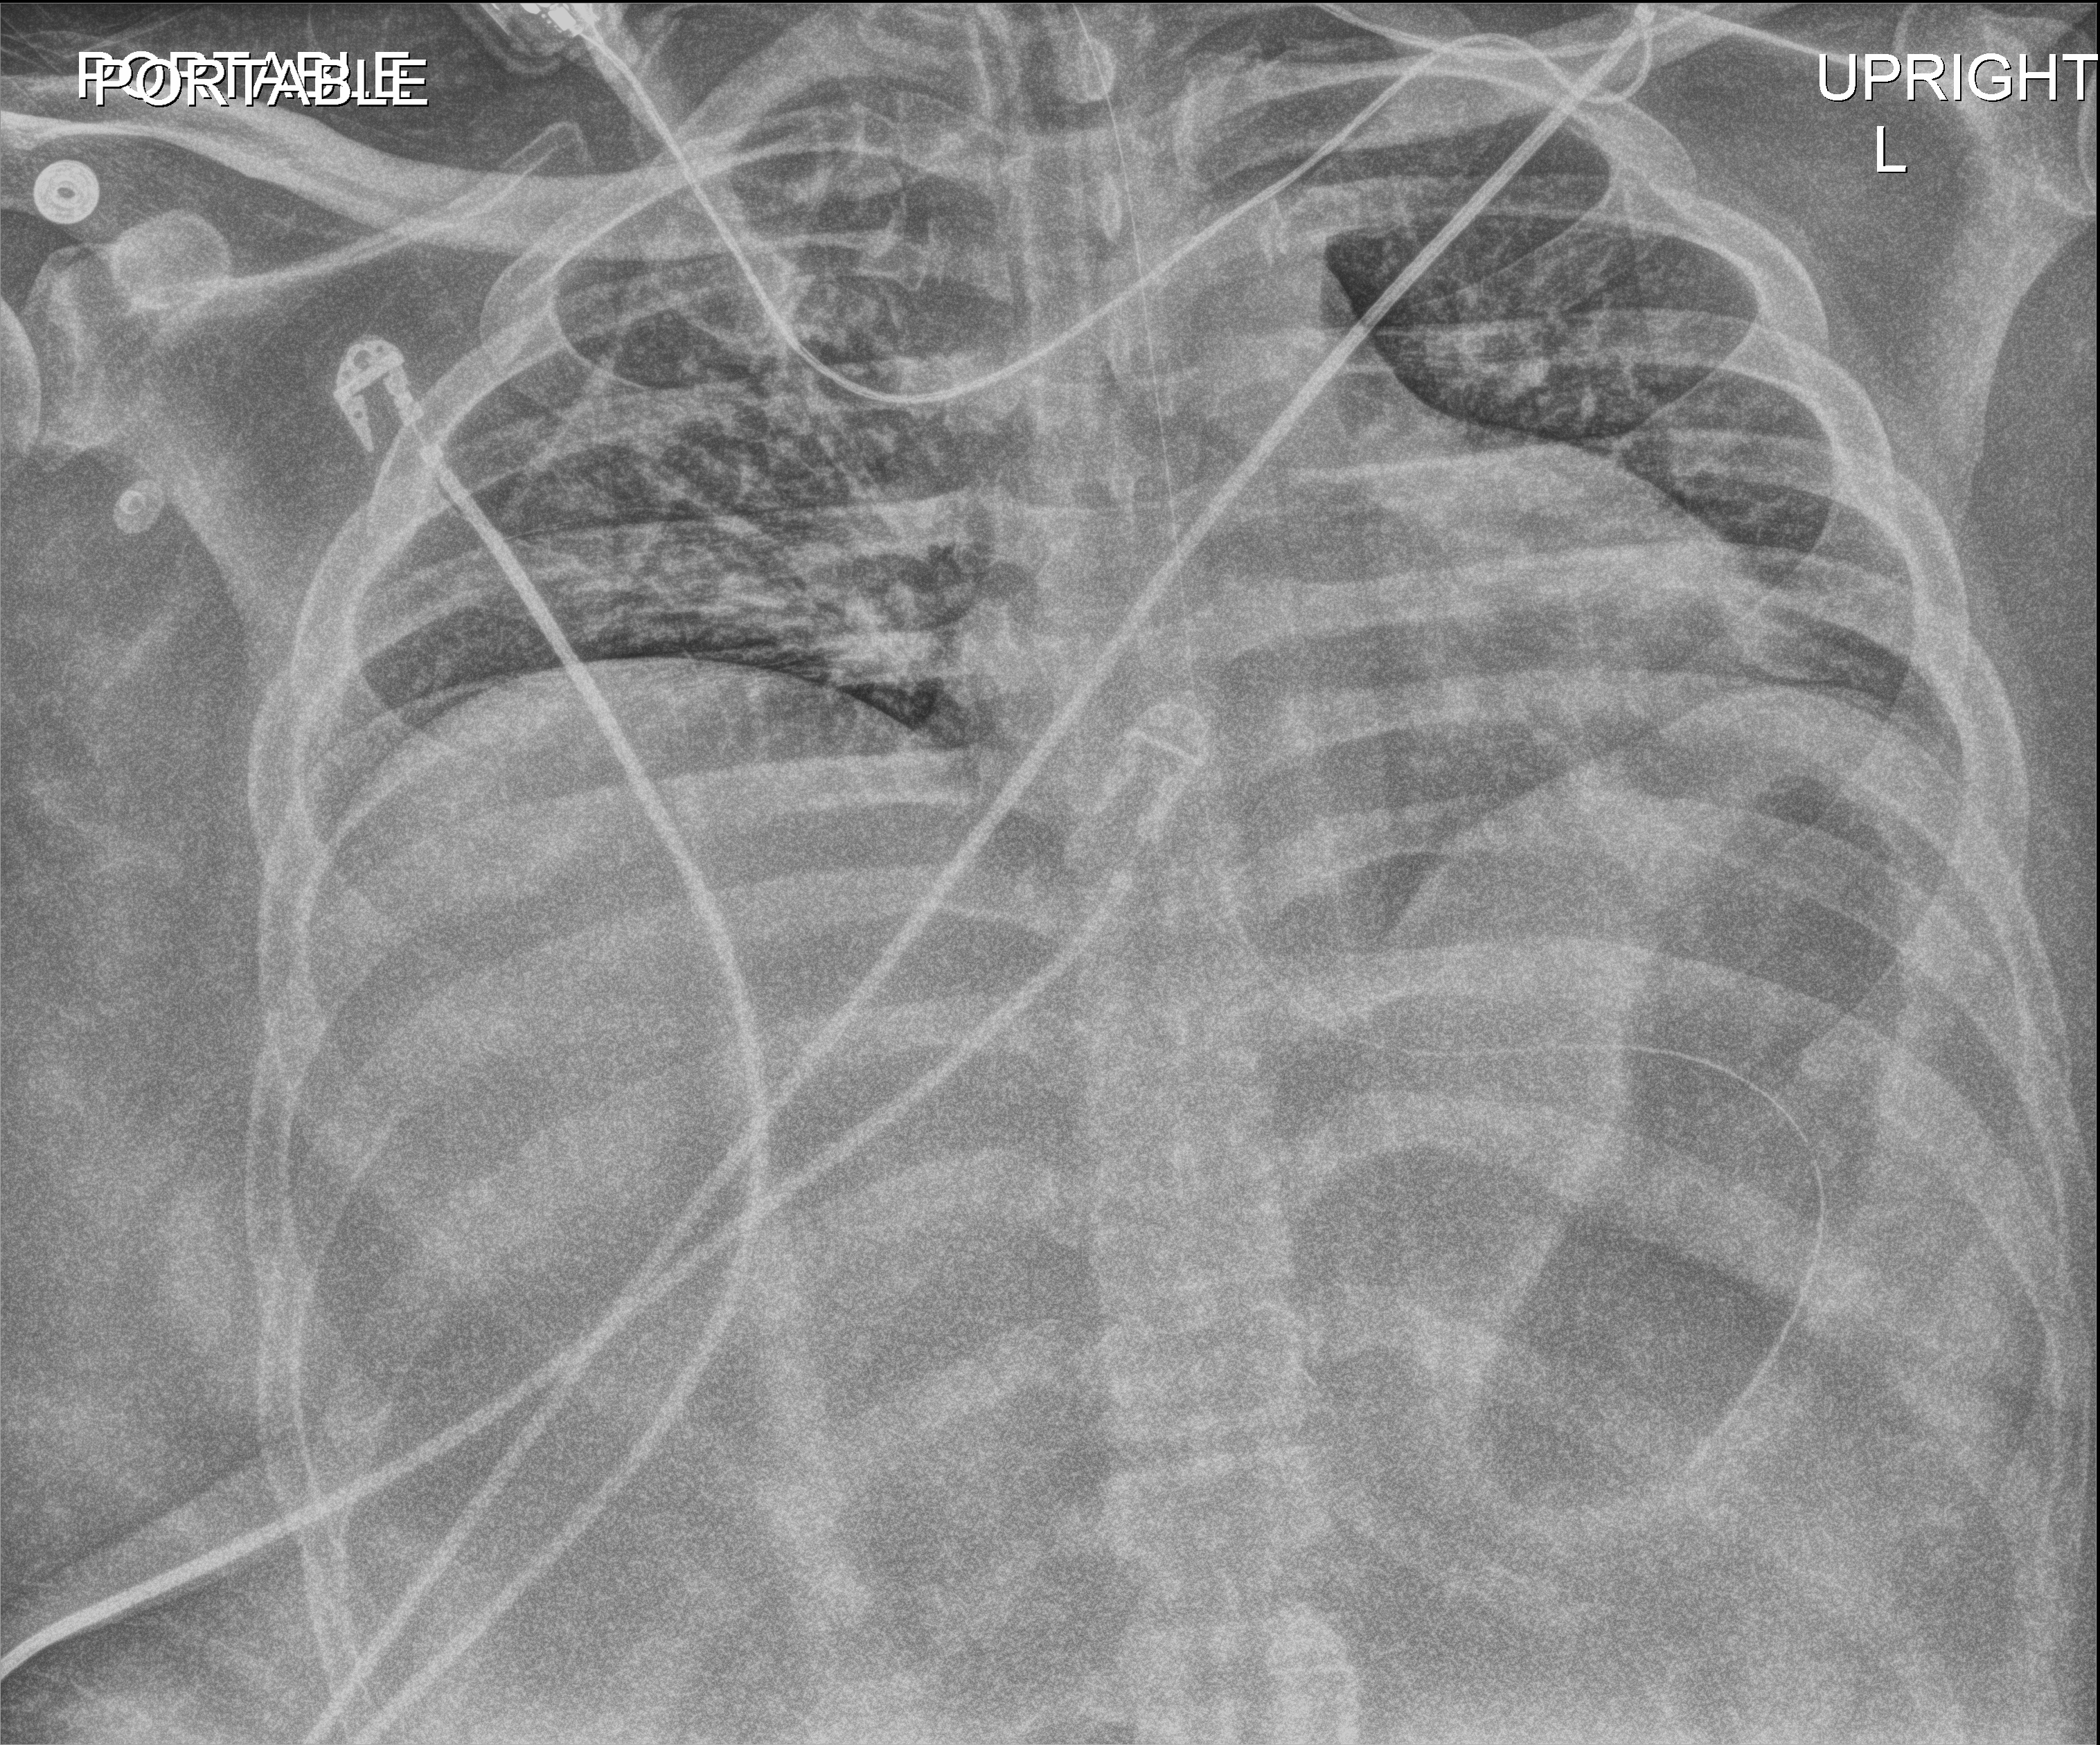
Portable chest radiograph; anteroposterior (AP) projection. Patient hospitalised with COVID-19; male, aged 18–59 years.
Hospital-stay facts (about this admission, not read from this image; timing relative to this image not recorded): mechanically ventilated during this hospital stay: yes; hypertension (admission record): no.